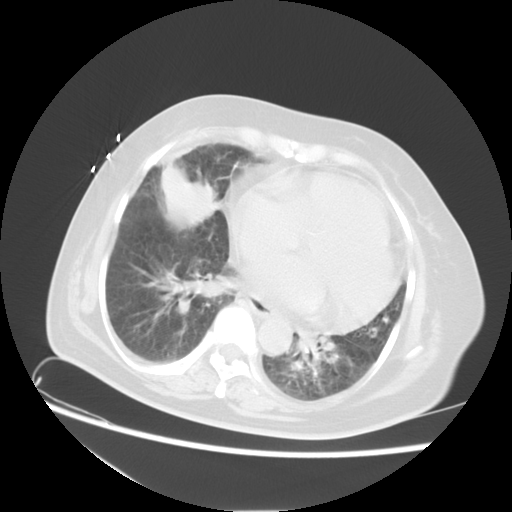
Chest CT, one axial slice. Position 7 of 23 along the scan axis. Reconstruction kernel STANDARD. Lung window (W 1500 / L -600 HU). 5 mm slice thickness. 512 × 512 image matrix, field of view 350 × 350 mm. Female patient, age 67 years. From the clinical record (not read from this slice): clinical TNM (as recorded): T2a N3 M1a.
Outlined on this slice (rectangle marked by the reading radiologist):
- lung tumour (recorded histology: adenocarcinoma): bounding box [x1, y1, x2, y2] px = [160, 161, 220, 230]